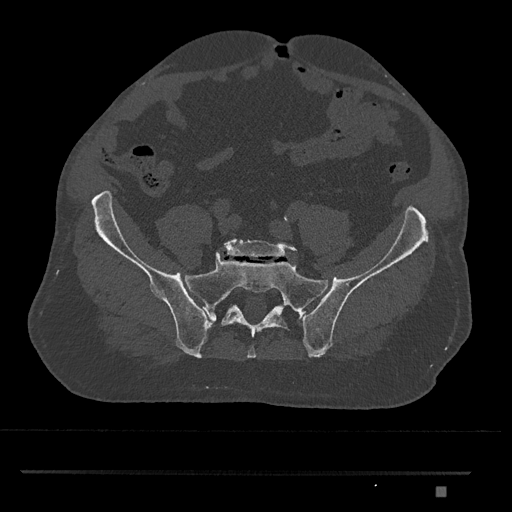
CT including the spine, one axial slice. Position 504 of 1134 along the scan axis. Bone window (W 1800 / L 400 HU). 0.5 mm slice thickness. 512 × 512 image matrix, field of view 429 × 429 mm. Male patient, age 65 years. Case-level facts recorded for this patient, not image findings: primary cancer: prostate.
Outlined on this slice (semi-automatic segmentation, software-assisted and operator-edited):
- L5 vertebra: box from (x=223, y=239) to (x=297, y=258) px